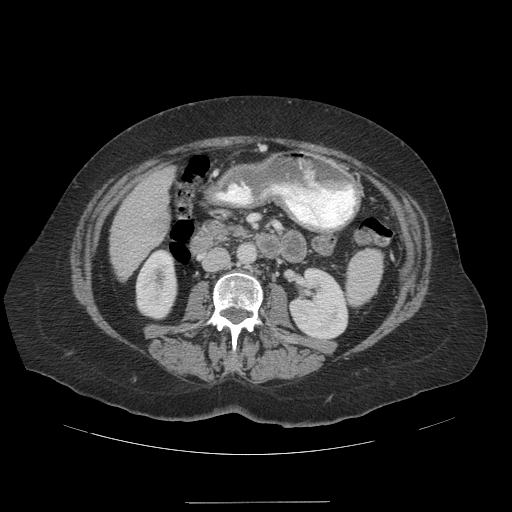
Contrast-enhanced abdominal CT (liver protocol), one axial slice. Position 41 of 99 along the scan axis. Reconstruction kernel STANDARD. Soft-tissue window (W 400 / L 40 HU). 2.5 mm slice thickness. 512 × 512 image matrix, field of view 440 × 440 mm. From the clinical record (not read from this slice): diagnosis: hepatocellular carcinoma (patient treated with transarterial chemoembolisation; whether this scan precedes or follows treatment is not stated here); TNM stage (as recorded): Stage-IVA; Child-Pugh class: A; tumour nodularity: multinodular.
Outlined on this slice (semi-automatic segmentation, software-assisted and operator-edited):
- liver parenchyma outside the tumour (the mass and vessels are separate outlines, so this box may not span the whole liver): bounding box <110,168,174,278> (left, top, right, bottom; pixels)